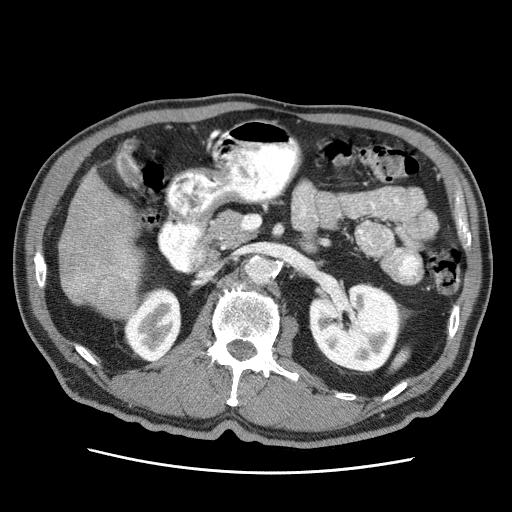
Contrast-enhanced abdominal CT (liver protocol), one axial slice; slice 12 of 75 in the series (ordered by position); reconstruction kernel STANDARD; 120 kVp; soft-tissue window (W 400 / L 40 HU); 2.5 mm slice thickness; 512 × 512 image matrix, field of view 360 × 360 mm. Case-level facts recorded for this patient, not image findings: diagnosis: hepatocellular carcinoma (patient treated with transarterial chemoembolisation; whether this scan precedes or follows treatment is not stated here); TNM stage (as recorded): Stage-IIIA; Child-Pugh class: A; tumour nodularity: multinodular.
Outlined on this slice (semi-automatic segmentation, software-assisted and operator-edited):
- liver parenchyma outside the tumour (the mass and vessels are separate outlines, so this box may not span the whole liver): box from (x=58, y=170) to (x=140, y=318) px
- mass: (x=59, y=178)–(x=131, y=289)
- liver vessels: (x=123, y=274)–(x=128, y=278)